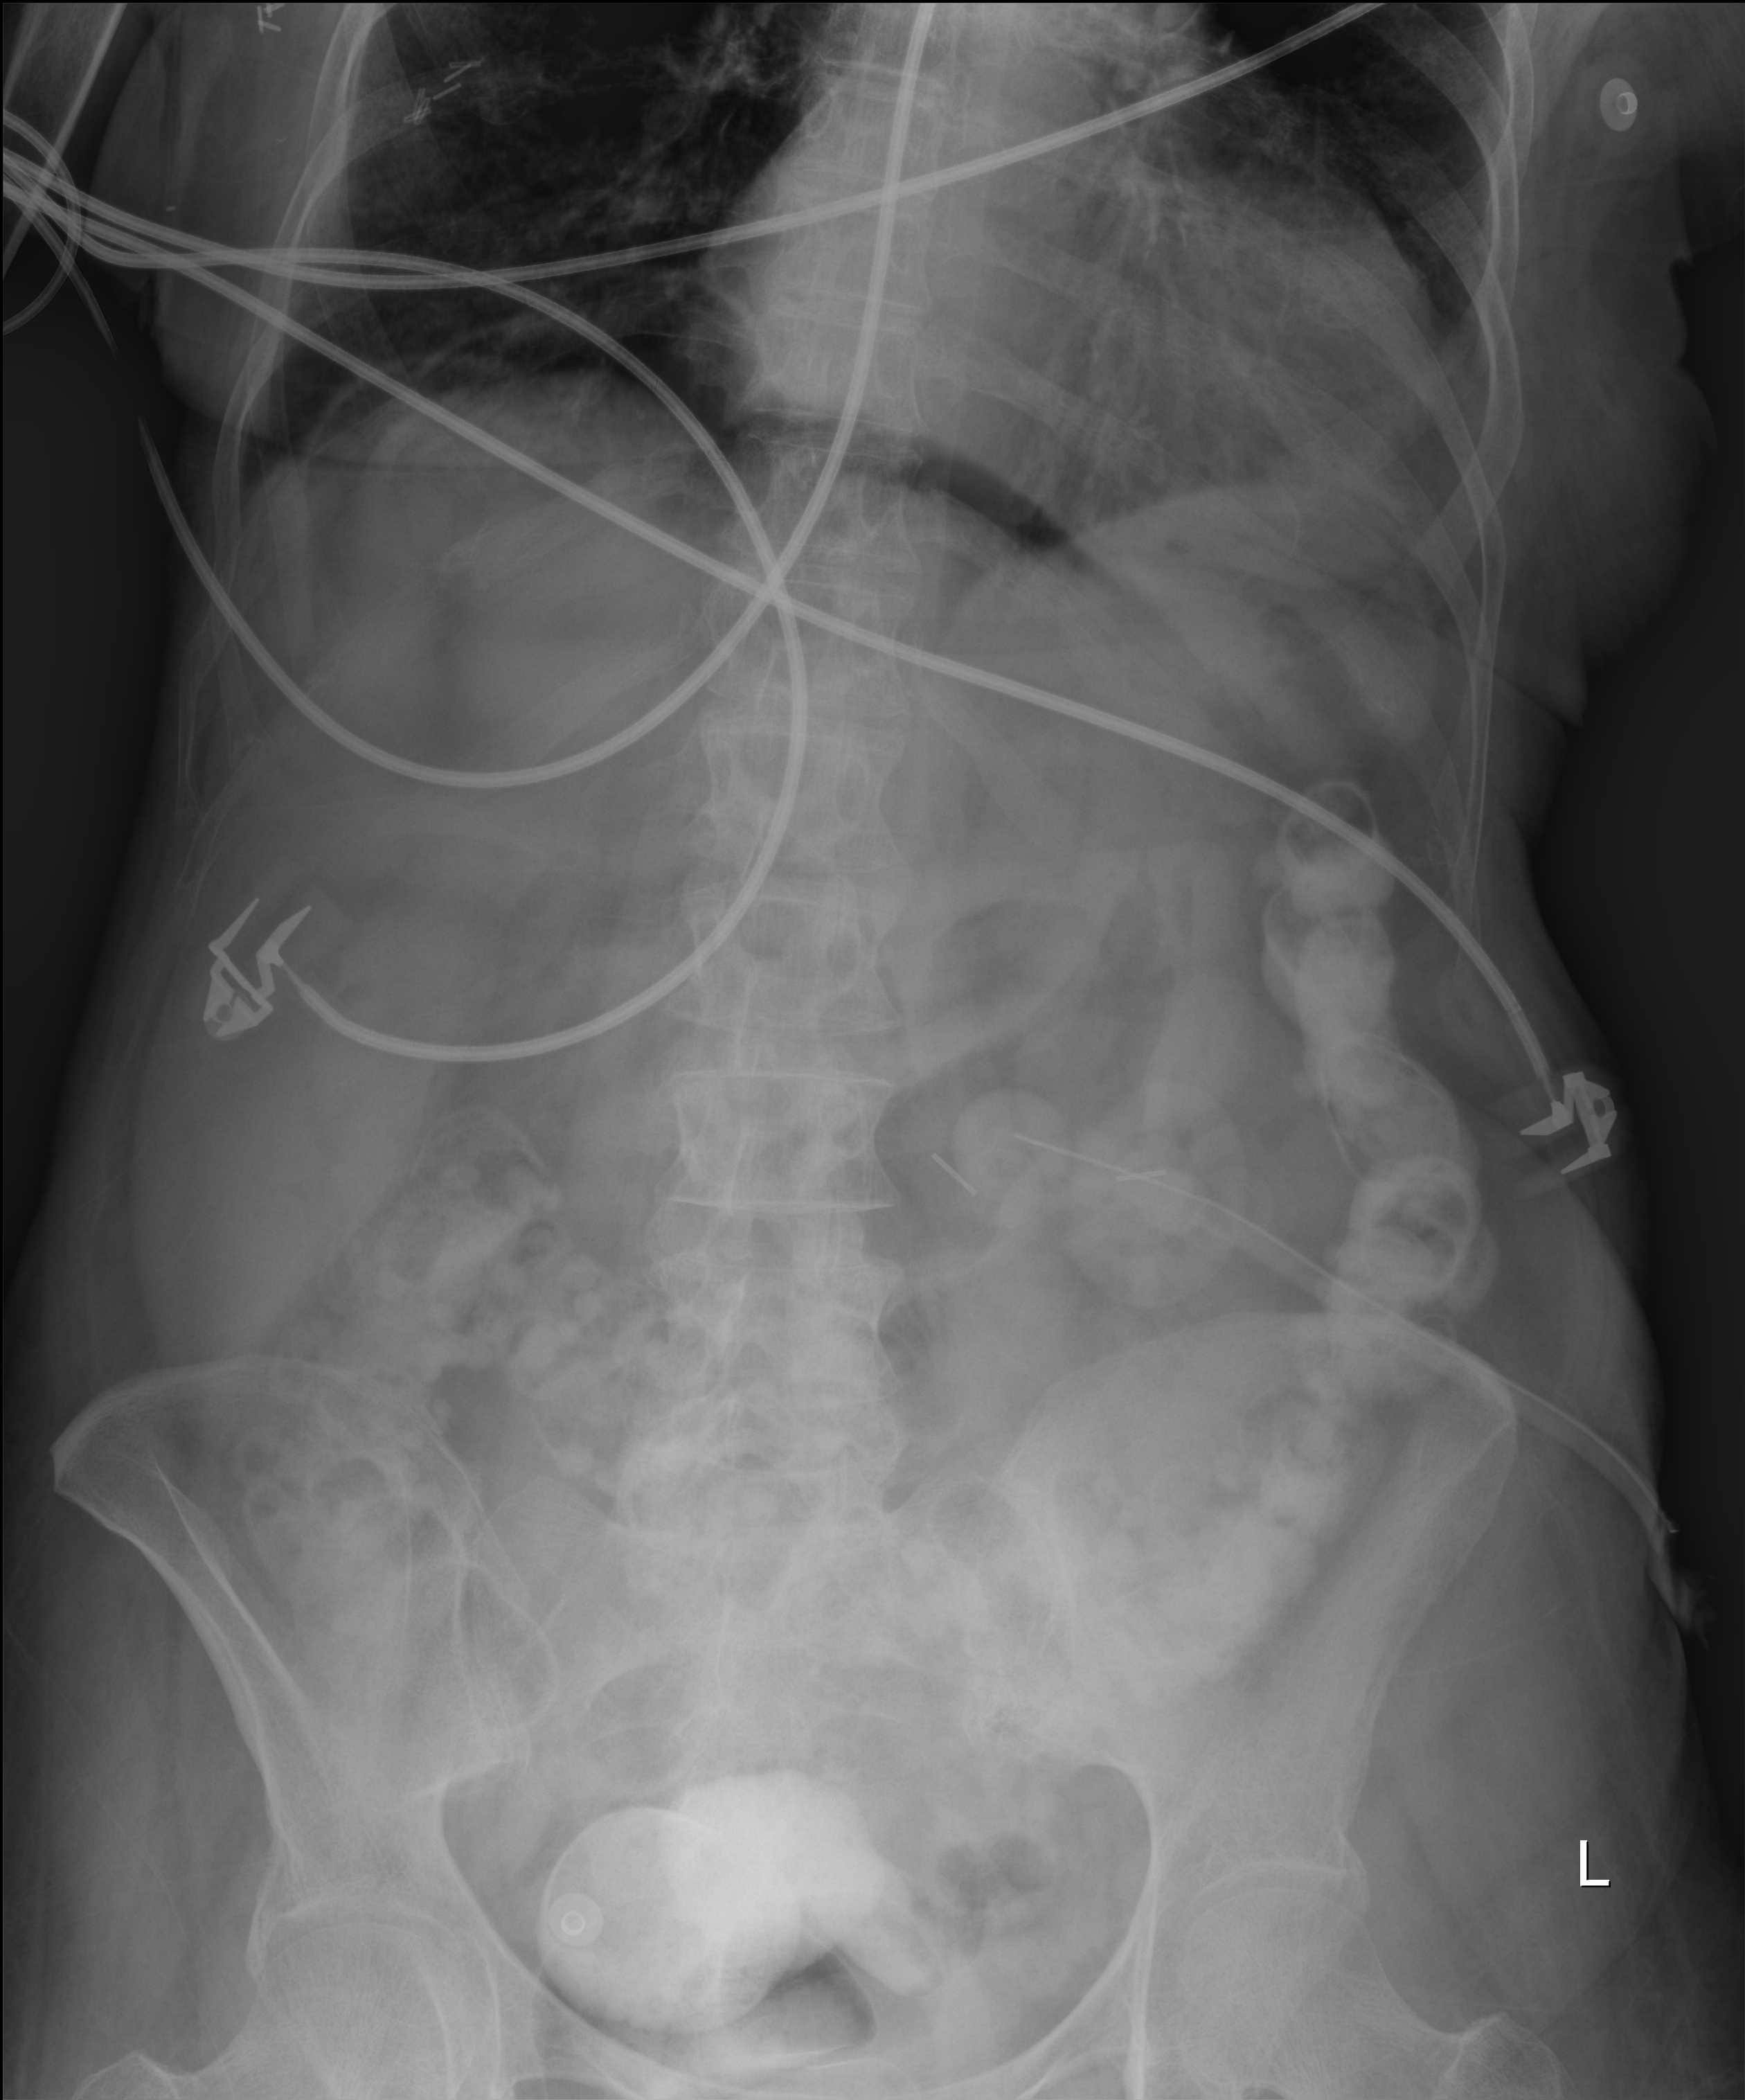
Bedside abdomen radiograph (digital radiography), anteroposterior (AP) projection. Female patient hospitalised with COVID-19, age 60–74 years.
Hospital-stay facts (about this admission, not read from this image; timing relative to this image not recorded): admitted to intensive care during this hospital stay: yes; other chronic lung disease (admission record): no; smoking status (admission record): former.